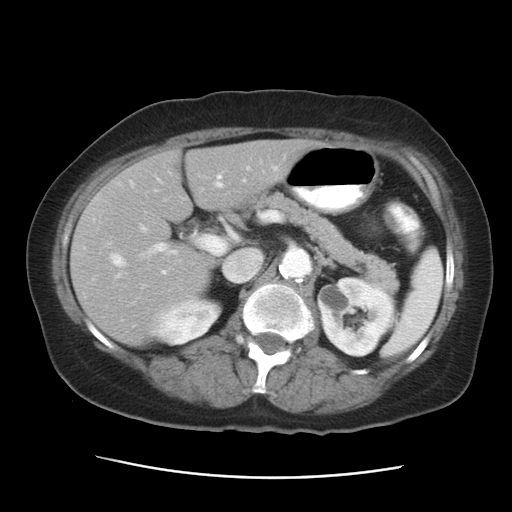
Contrast-enhanced abdominal CT, one axial slice; slice 16 of 29 in the series (ordered by position); reconstruction kernel STANDARD; 120 kVp; intravenous contrast given; soft-tissue window (W 400 / L 40 HU); 512 × 512 image matrix. Female patient, age 64 years. From the clinical record (not read from this slice): diagnosis: colorectal cancer liver metastases, imaged before liver resection; multiple liver metastases: no; largest metastasis: 2.5 cm; disease in both lobes: no.
Outlined on this slice (expert manual segmentation):
- hepatic veins: bounding box [x1, y1, x2, y2] px = [110, 167, 276, 274]
- liver: [71, 140, 316, 344]
- planned liver remnant (the part of the liver to remain after resection): [71, 139, 316, 316]
- portal vein (with intrahepatic branches): [116, 182, 237, 277]